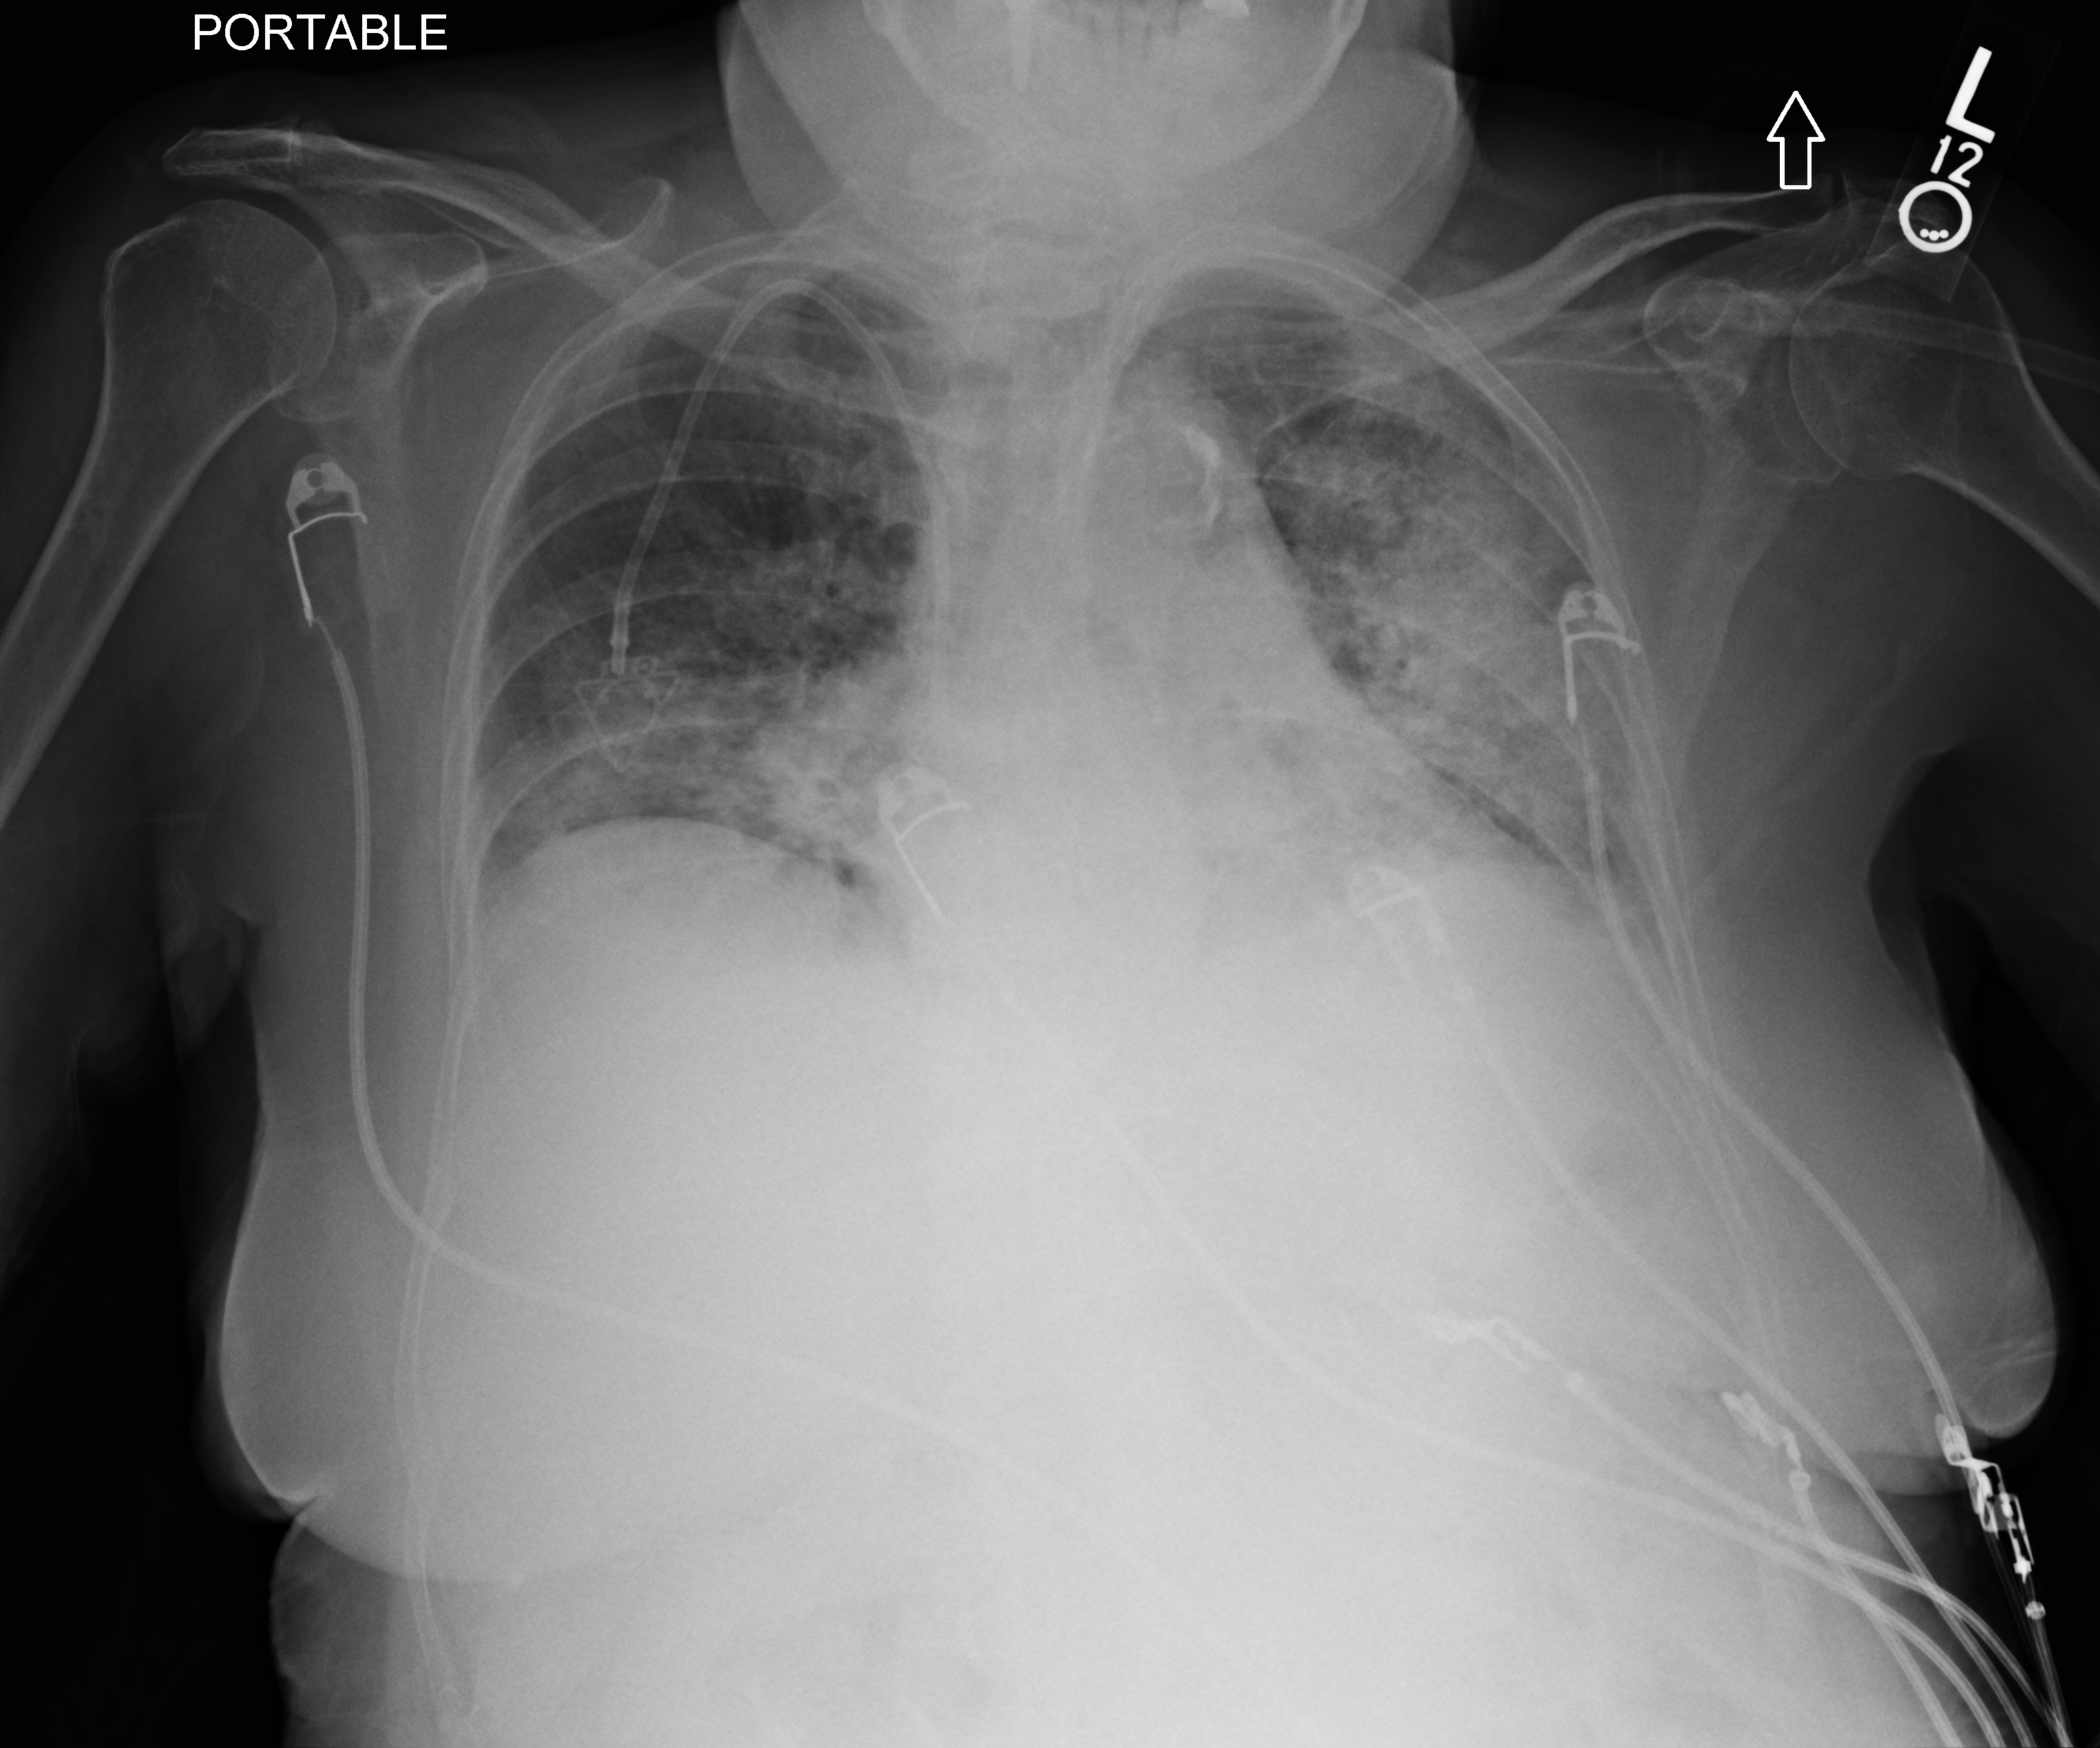
Chest X-ray (portable), anteroposterior (AP) projection. Female patient hospitalised with COVID-19, age 75–90 years.
Admission-level facts for this patient (not findings on this image; timing relative to this image not recorded): mechanically ventilated during this hospital stay: no; admitted to intensive care during this hospital stay: no; diabetes (admission record): no.